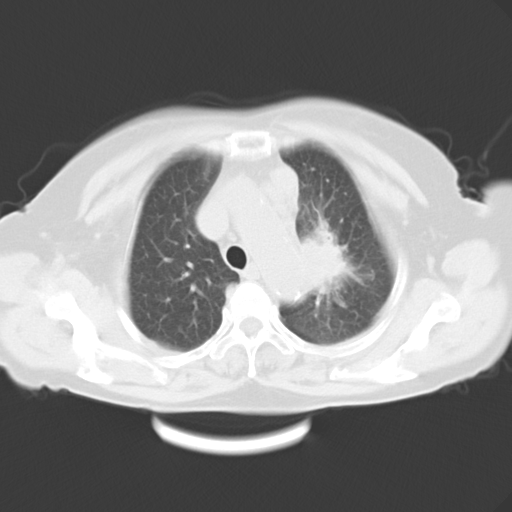
Chest CT, one axial slice; slice 21 of 26 in the series (ordered by position); 120 kVp; lung window (W 1500 / L -600 HU); 10 mm slice thickness; 512 × 512 image matrix, field of view 353 × 353 mm. Patient: female, 71 years. Case-level facts recorded for this patient, not image findings: clinical TNM (as recorded): T3 N3 M0.
Outlined on this slice (rectangle marked by the reading radiologist):
- lung tumour (recorded histology: adenocarcinoma): bounding box <287,210,361,315> (left, top, right, bottom; pixels)